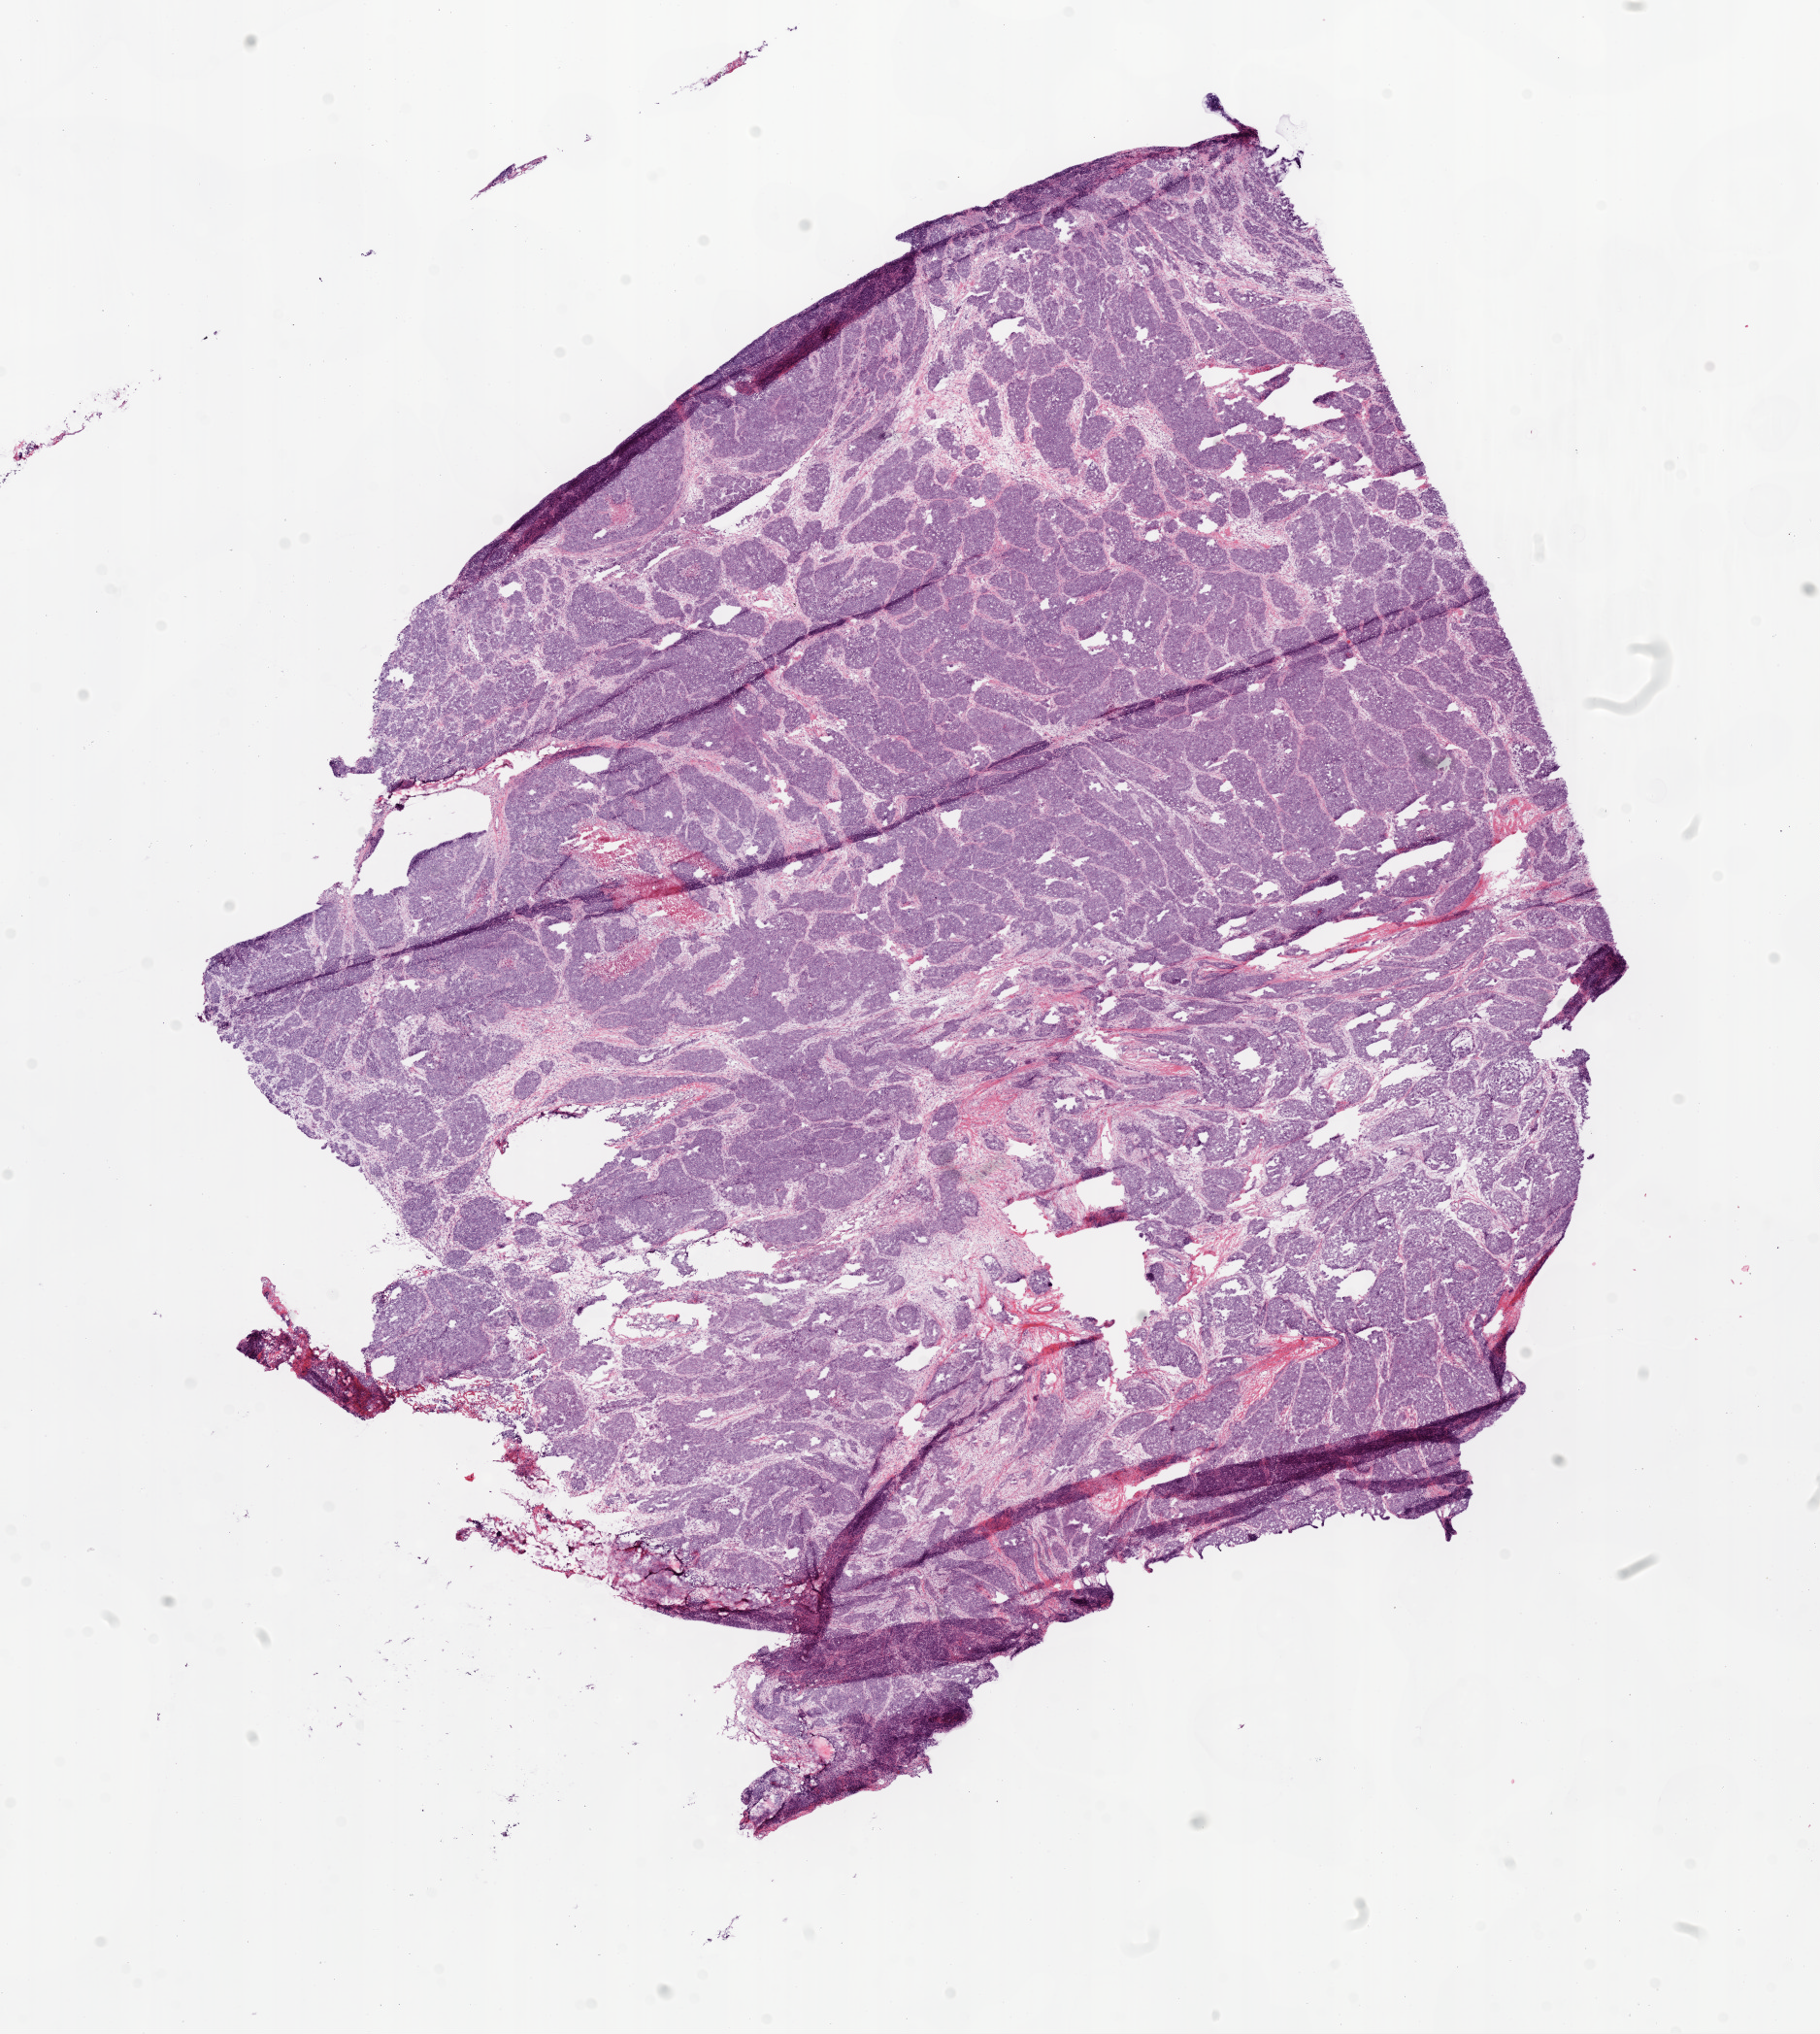
Whole-slide histology image, Hematoxylin and eosin (H&E) stained — a low-resolution overview of the entire scanned area, about 15.0 x 16.8 mm (slide scanned at 20x), frozen section, sample: primary tumour, ovary. Female, age 76 years at initial diagnosis. Histologic grade: G3 (poorly differentiated). Slide review estimates, as recorded: tumour cells 85%, tumour nuclei 90%, normal cells 1%, stromal cells 9%, necrosis 5%.
Histologic diagnosis: Serous cystadenocarcinoma, NOS. FIGO stage: IIIC.